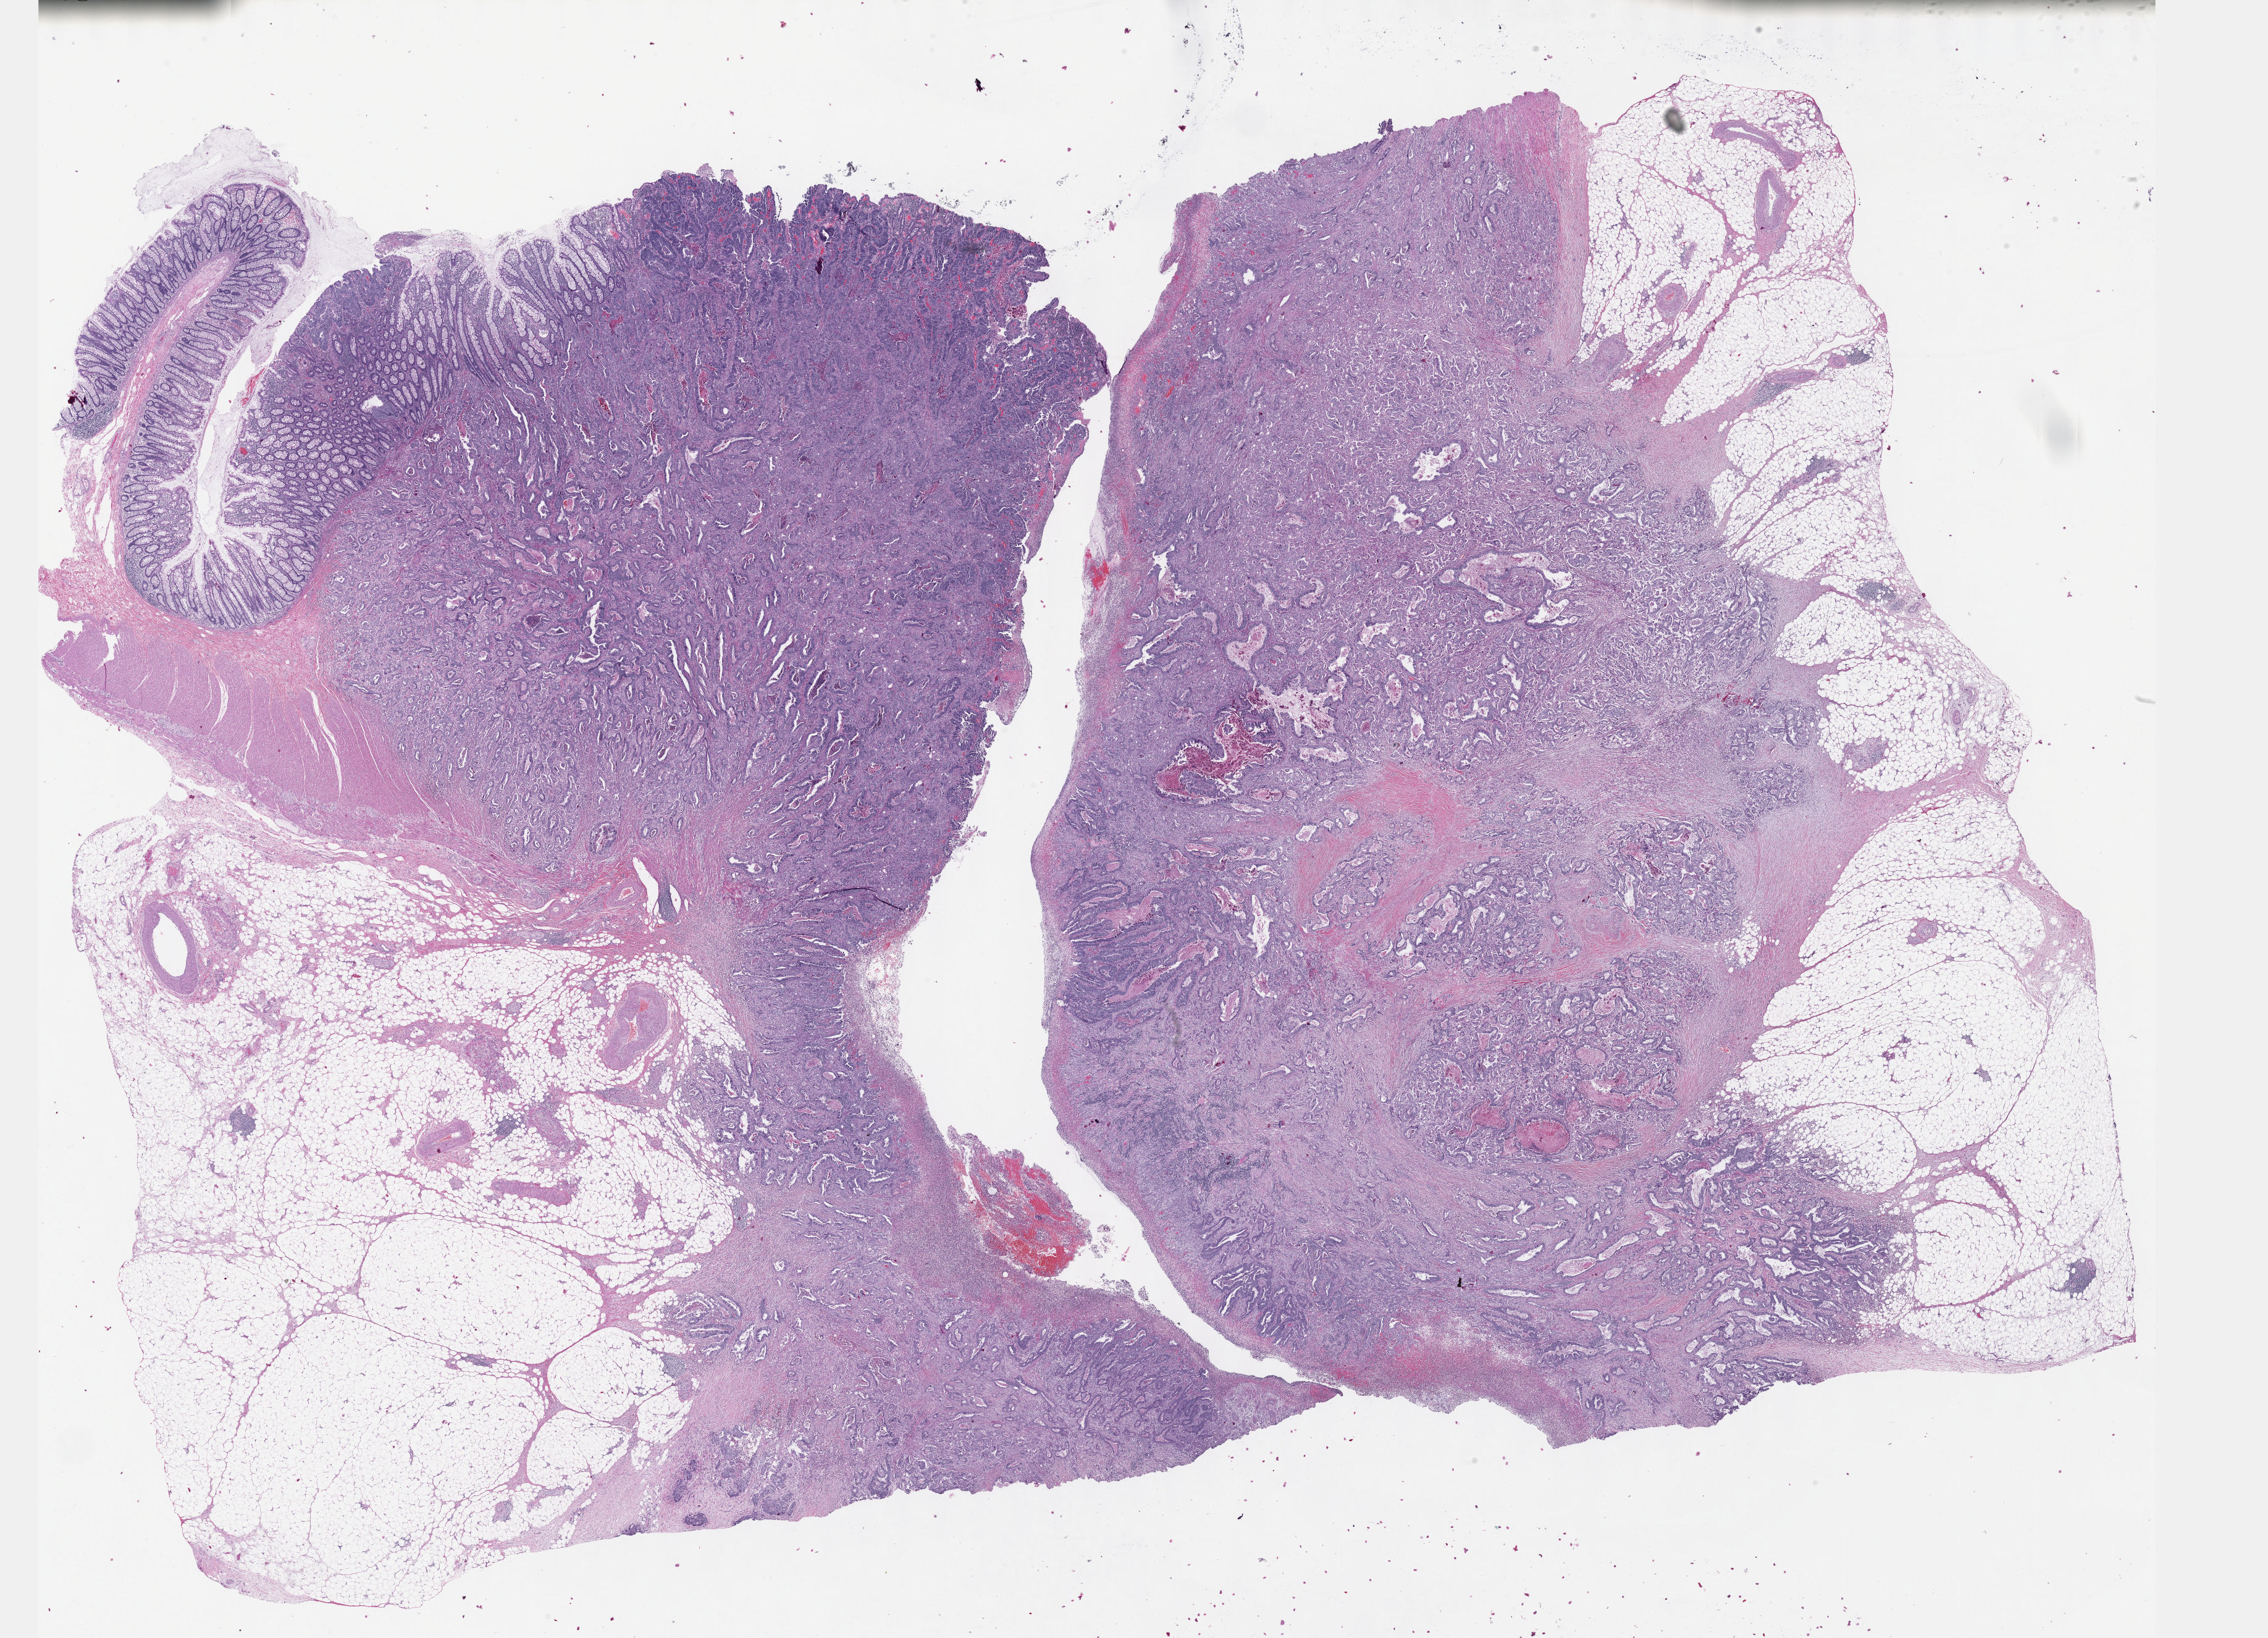
Digitized Hematoxylin and eosin (H&E) stained tissue section (whole slide) — shown as a low-resolution overview of the whole scanned area (about 29.7 x 21.4 mm, slide scanned at 40x), FFPE section, primary tumour sample from the colon. Female, age 71 years at initial diagnosis.
Pathologic diagnosis: Adenocarcinoma, NOS (transverse colon).